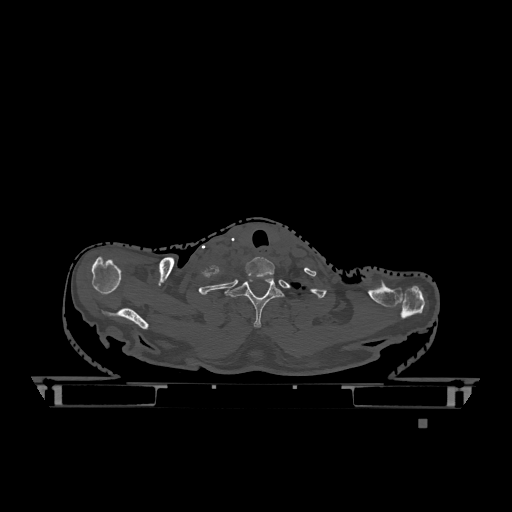
CT including the spine, one axial slice. Slice 1003 of 1317 in the series (ordered by position). Bone window (W 1800 / L 400 HU). 0.5 mm slice thickness. 512 × 512 image matrix, field of view 500 × 500 mm. Female patient, age 74 years. From the clinical record (not read from this slice): primary cancer: lung; vertebrae with lytic lesions (as recorded): T1, T4, T5, T6, L4, L5.
Outlined on this slice (semi-automatic segmentation, software-assisted and operator-edited):
- T1 vertebra: bounding box (x1, y1, x2, y2) in pixels: (226, 275, 284, 328)